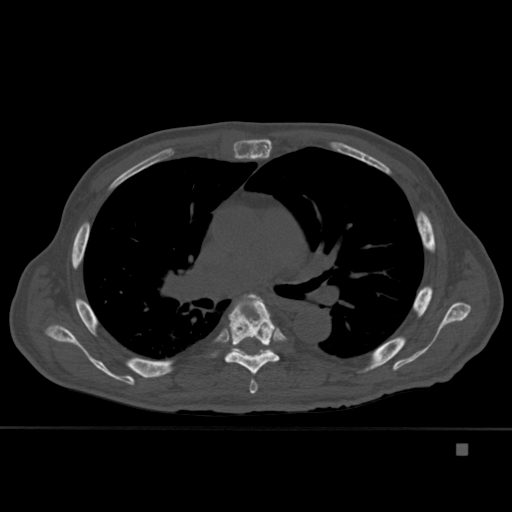
CT including the spine, one axial slice. Position 294 of 451 along the scan axis. Bone window (W 1800 / L 400 HU). 1.5 mm slice thickness. 512 × 512 image matrix, field of view 378 × 378 mm. Male patient, age 75 years. From the clinical record (not read from this slice): primary cancer: prostate.
Structures marked on this image (semi-automatically segmented with operator editing):
- T5 vertebra: bounding box [x1, y1, x2, y2] px = [242, 294, 263, 394]
- T6 vertebra: [224, 293, 280, 375]
- T7 vertebra: [234, 348, 271, 354]